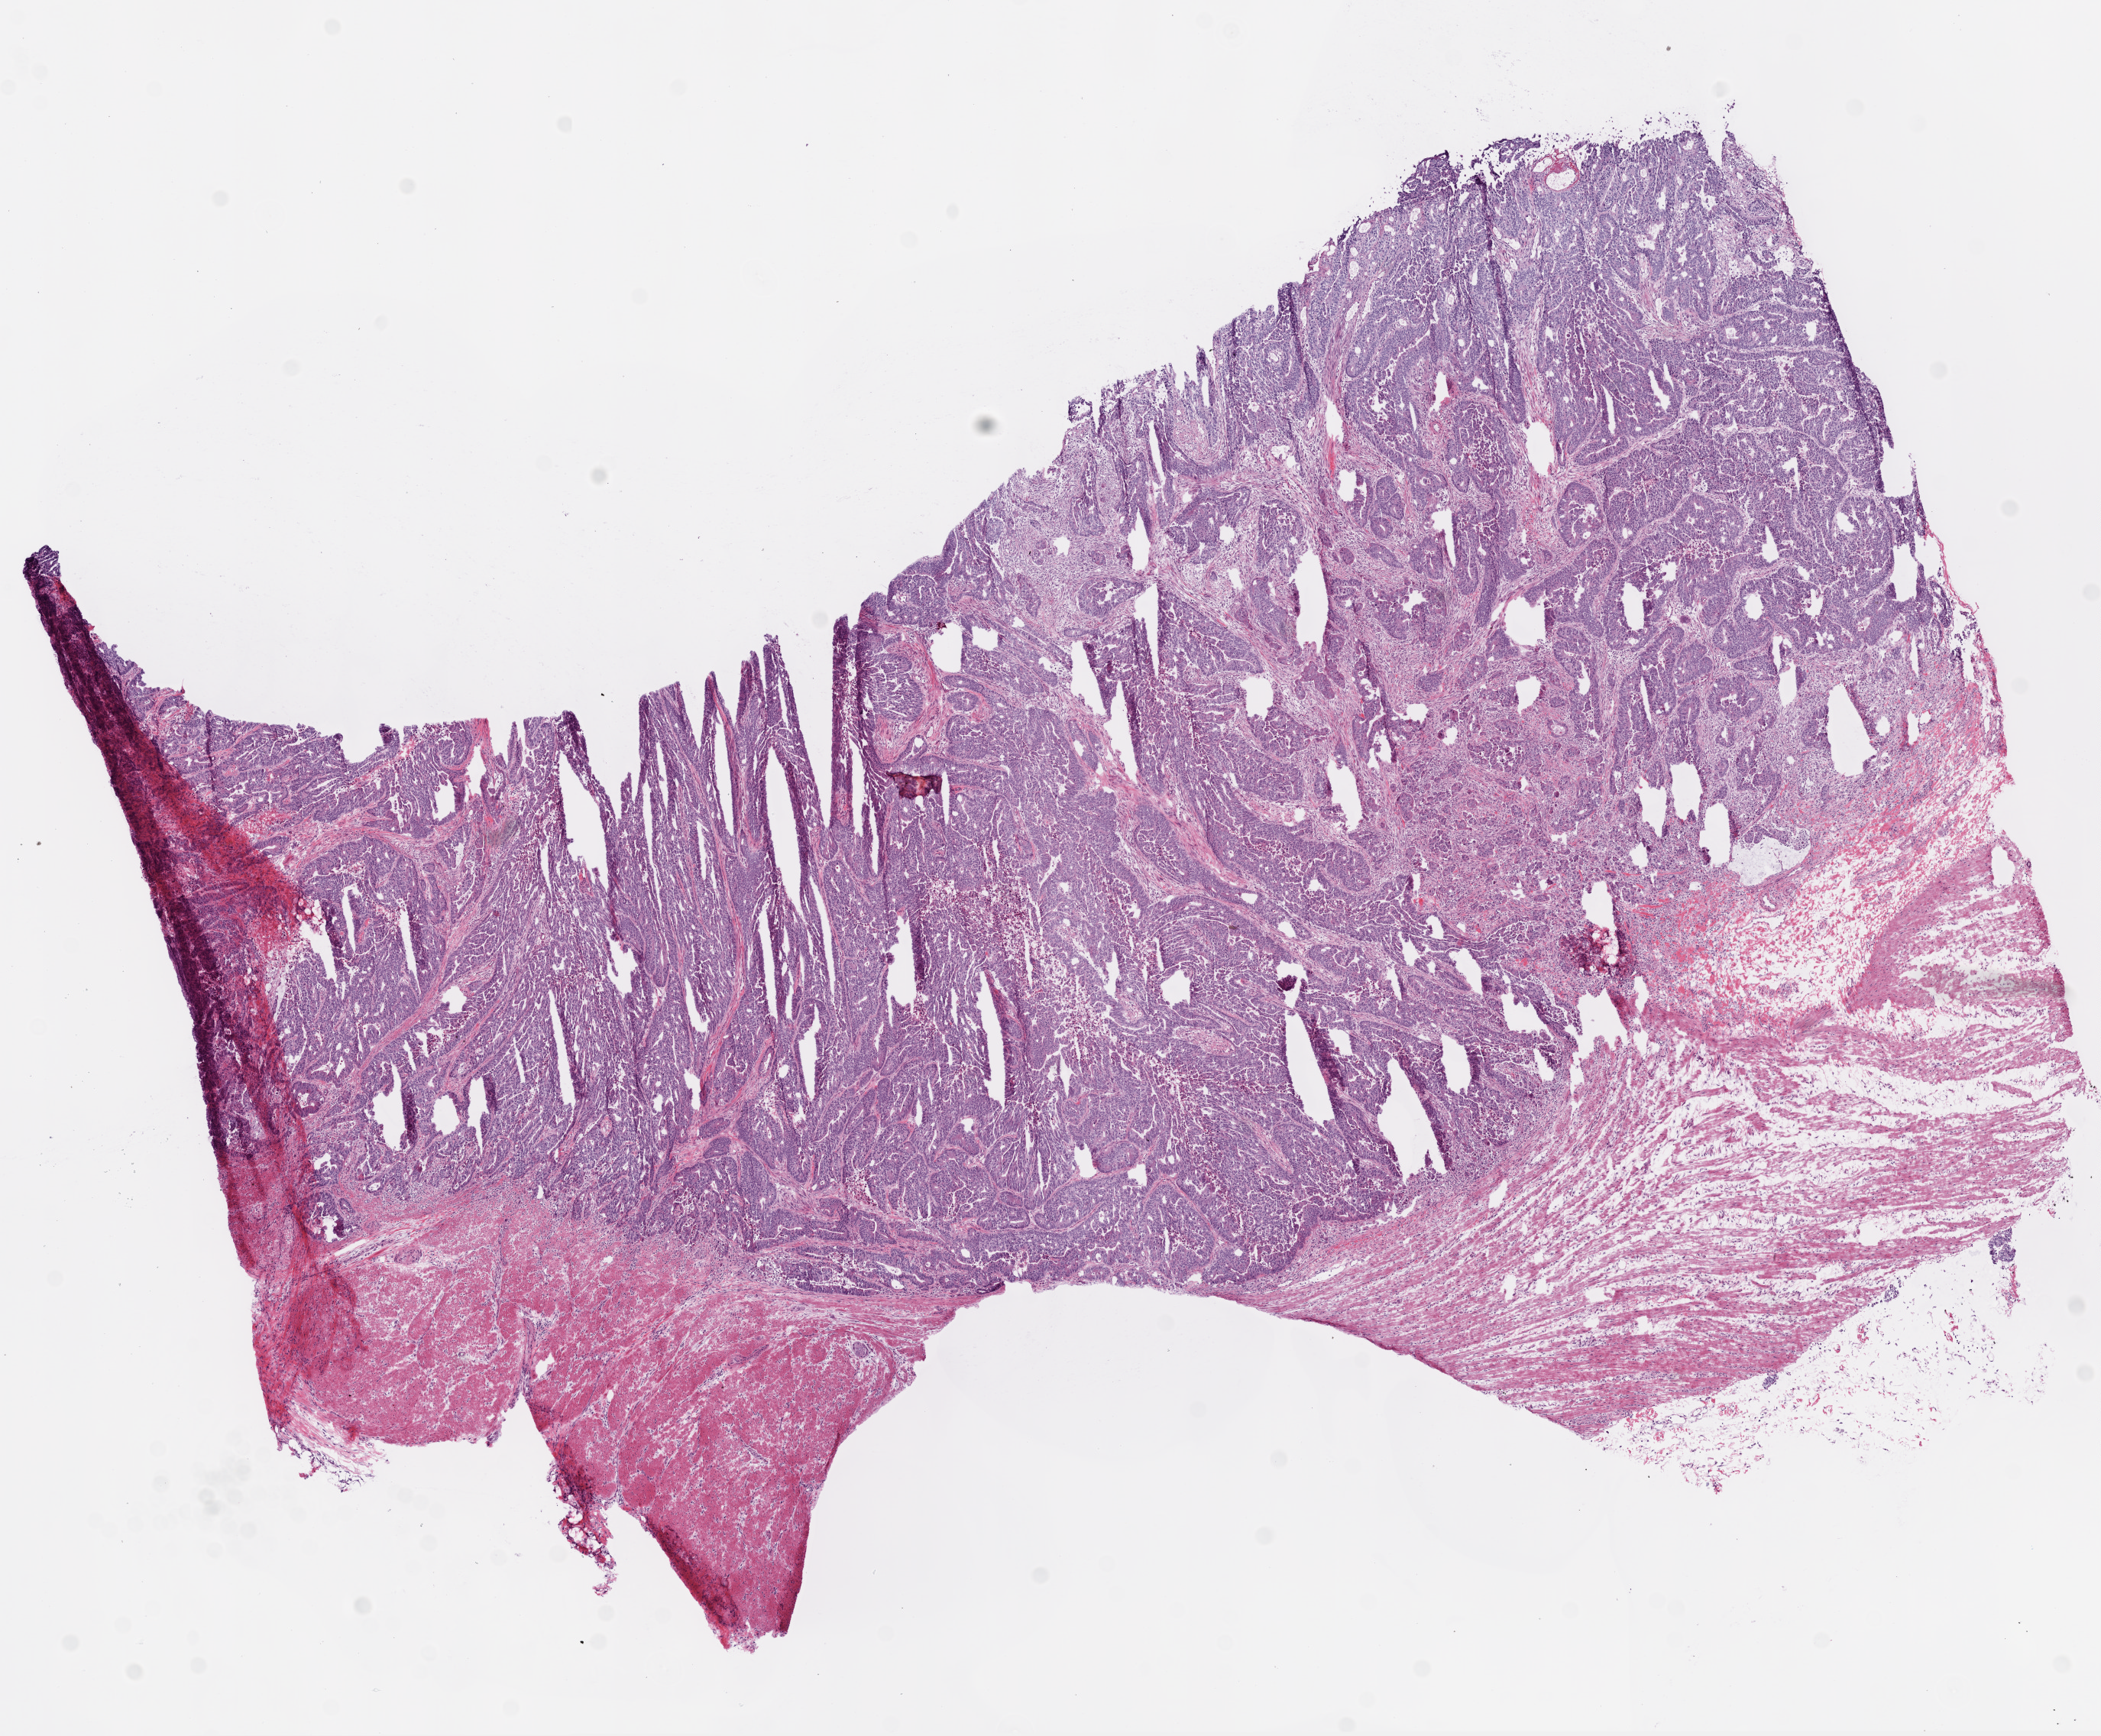
H&E whole-slide image, a low-resolution overview of the entire scanned area, about 11.0 x 9.1 mm (from a 20x scan), frozen section from the bottom of the tissue portion, colon, primary tumour sample. Patient: male, age at initial diagnosis 85 years. Composition of this section per pathologist review: tumour cells 75%, tumour nuclei 80%, normal cells 15%, stromal cells 5%, necrosis 5%.
* AJCC pathologic stage: IV
* lymph nodes positive (case pathology): 3 of 27 examined
* pathologic diagnosis: Adenocarcinoma, NOS (sigmoid colon)